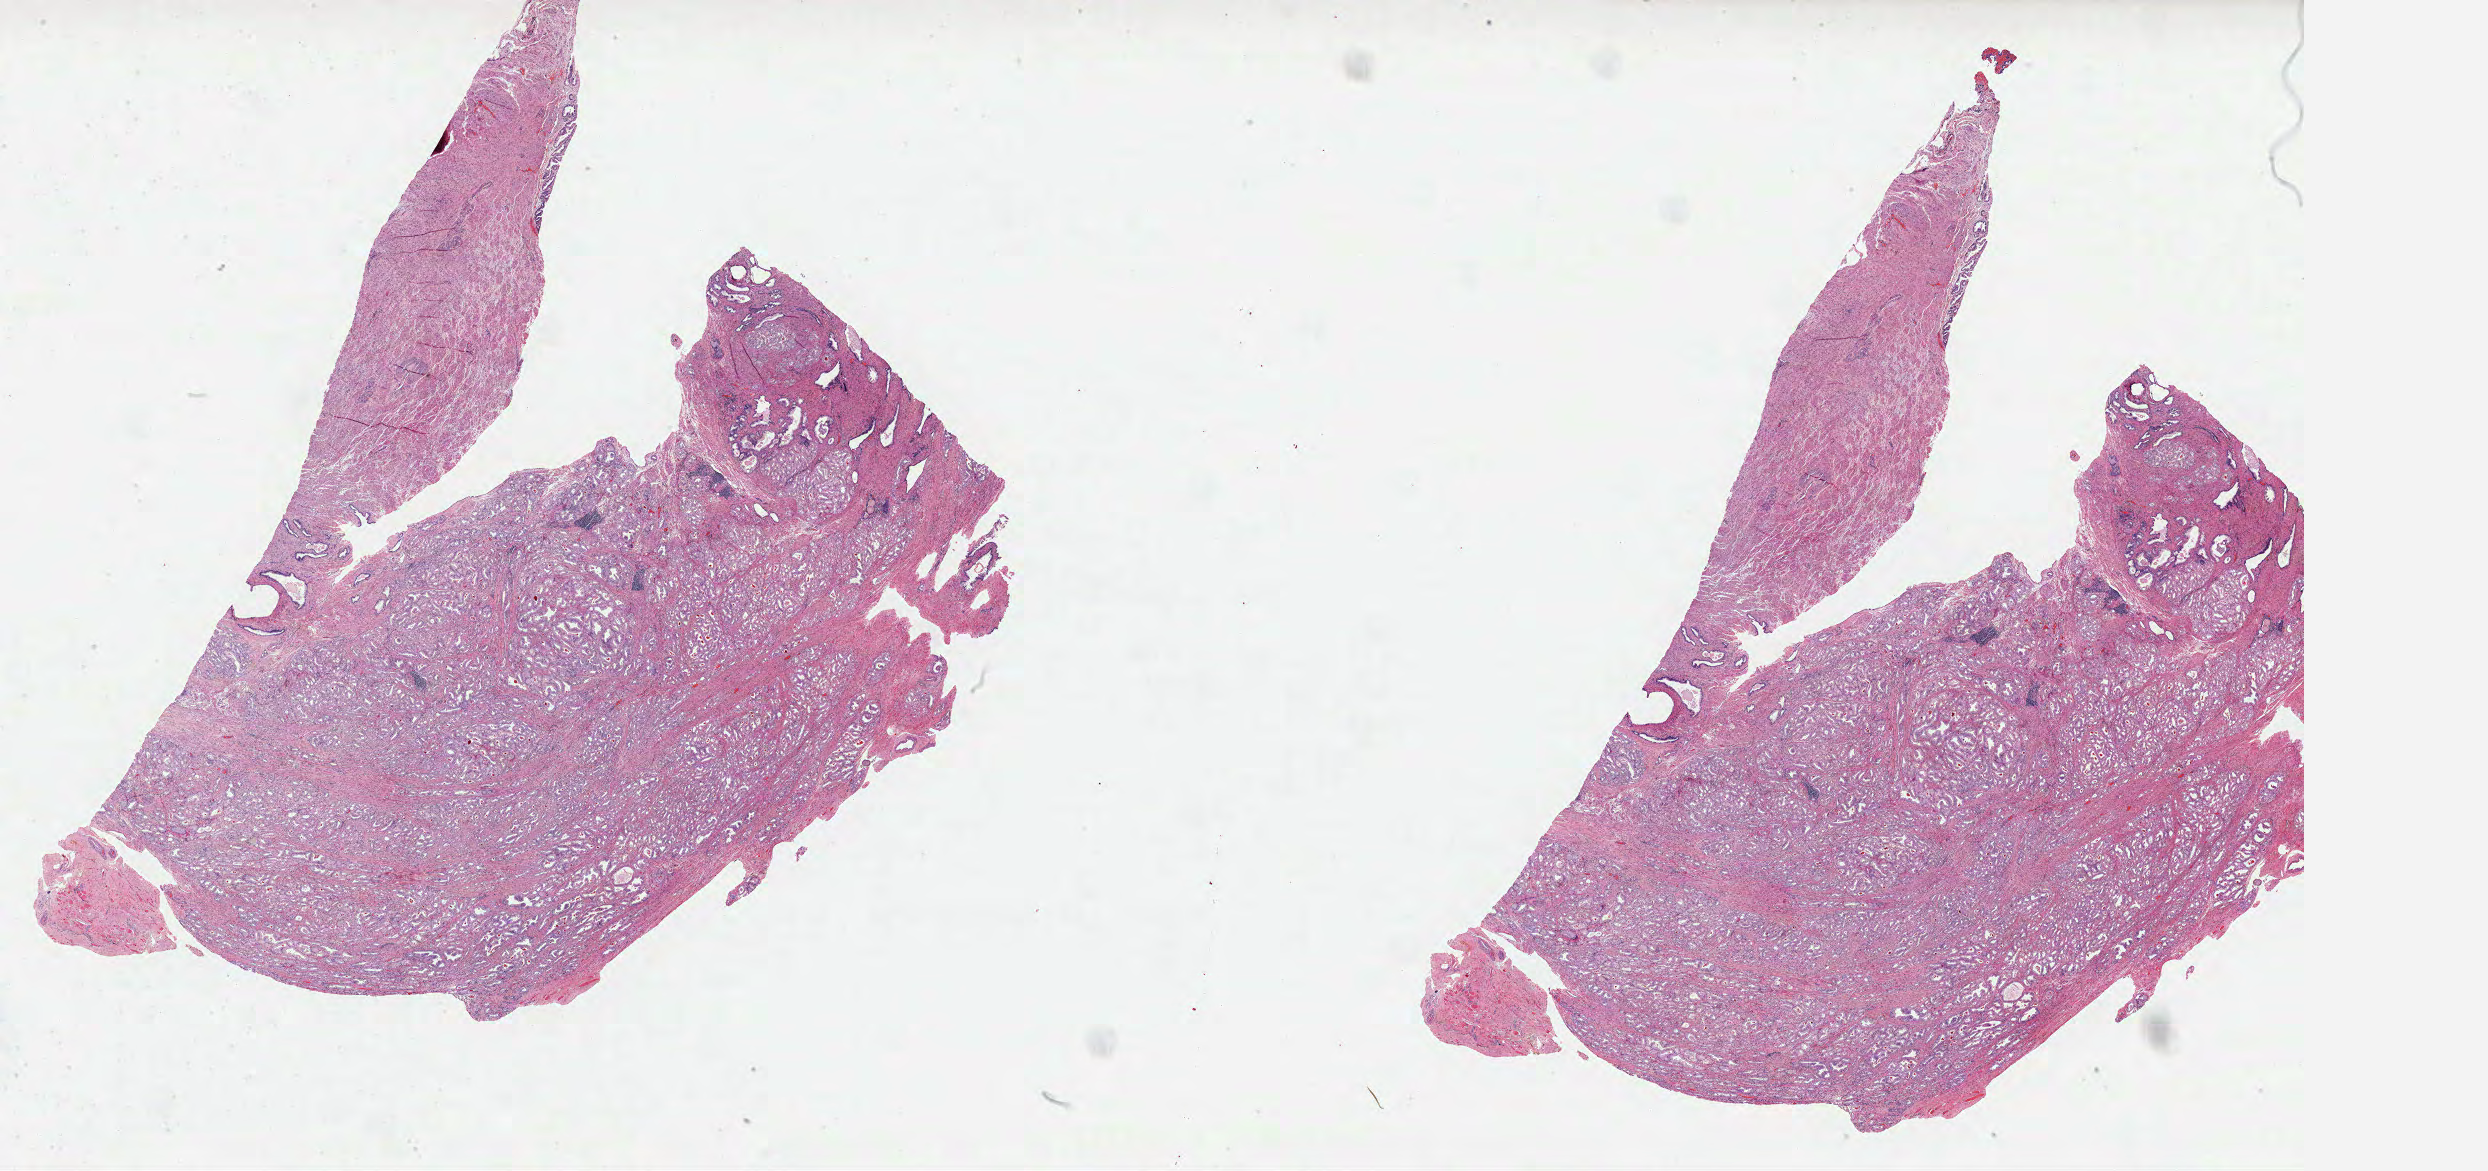
Hematoxylin and eosin (H&E) stained whole-slide image, low-resolution overview of the scanned area, about 40.1 x 18.9 mm. FFPE section. Primary tumour sample from the prostate. Male patient; age at initial diagnosis 67 years. Gleason score: 7 (3+4).
Histologic diagnosis: Acinar cell carcinoma (prostate gland).